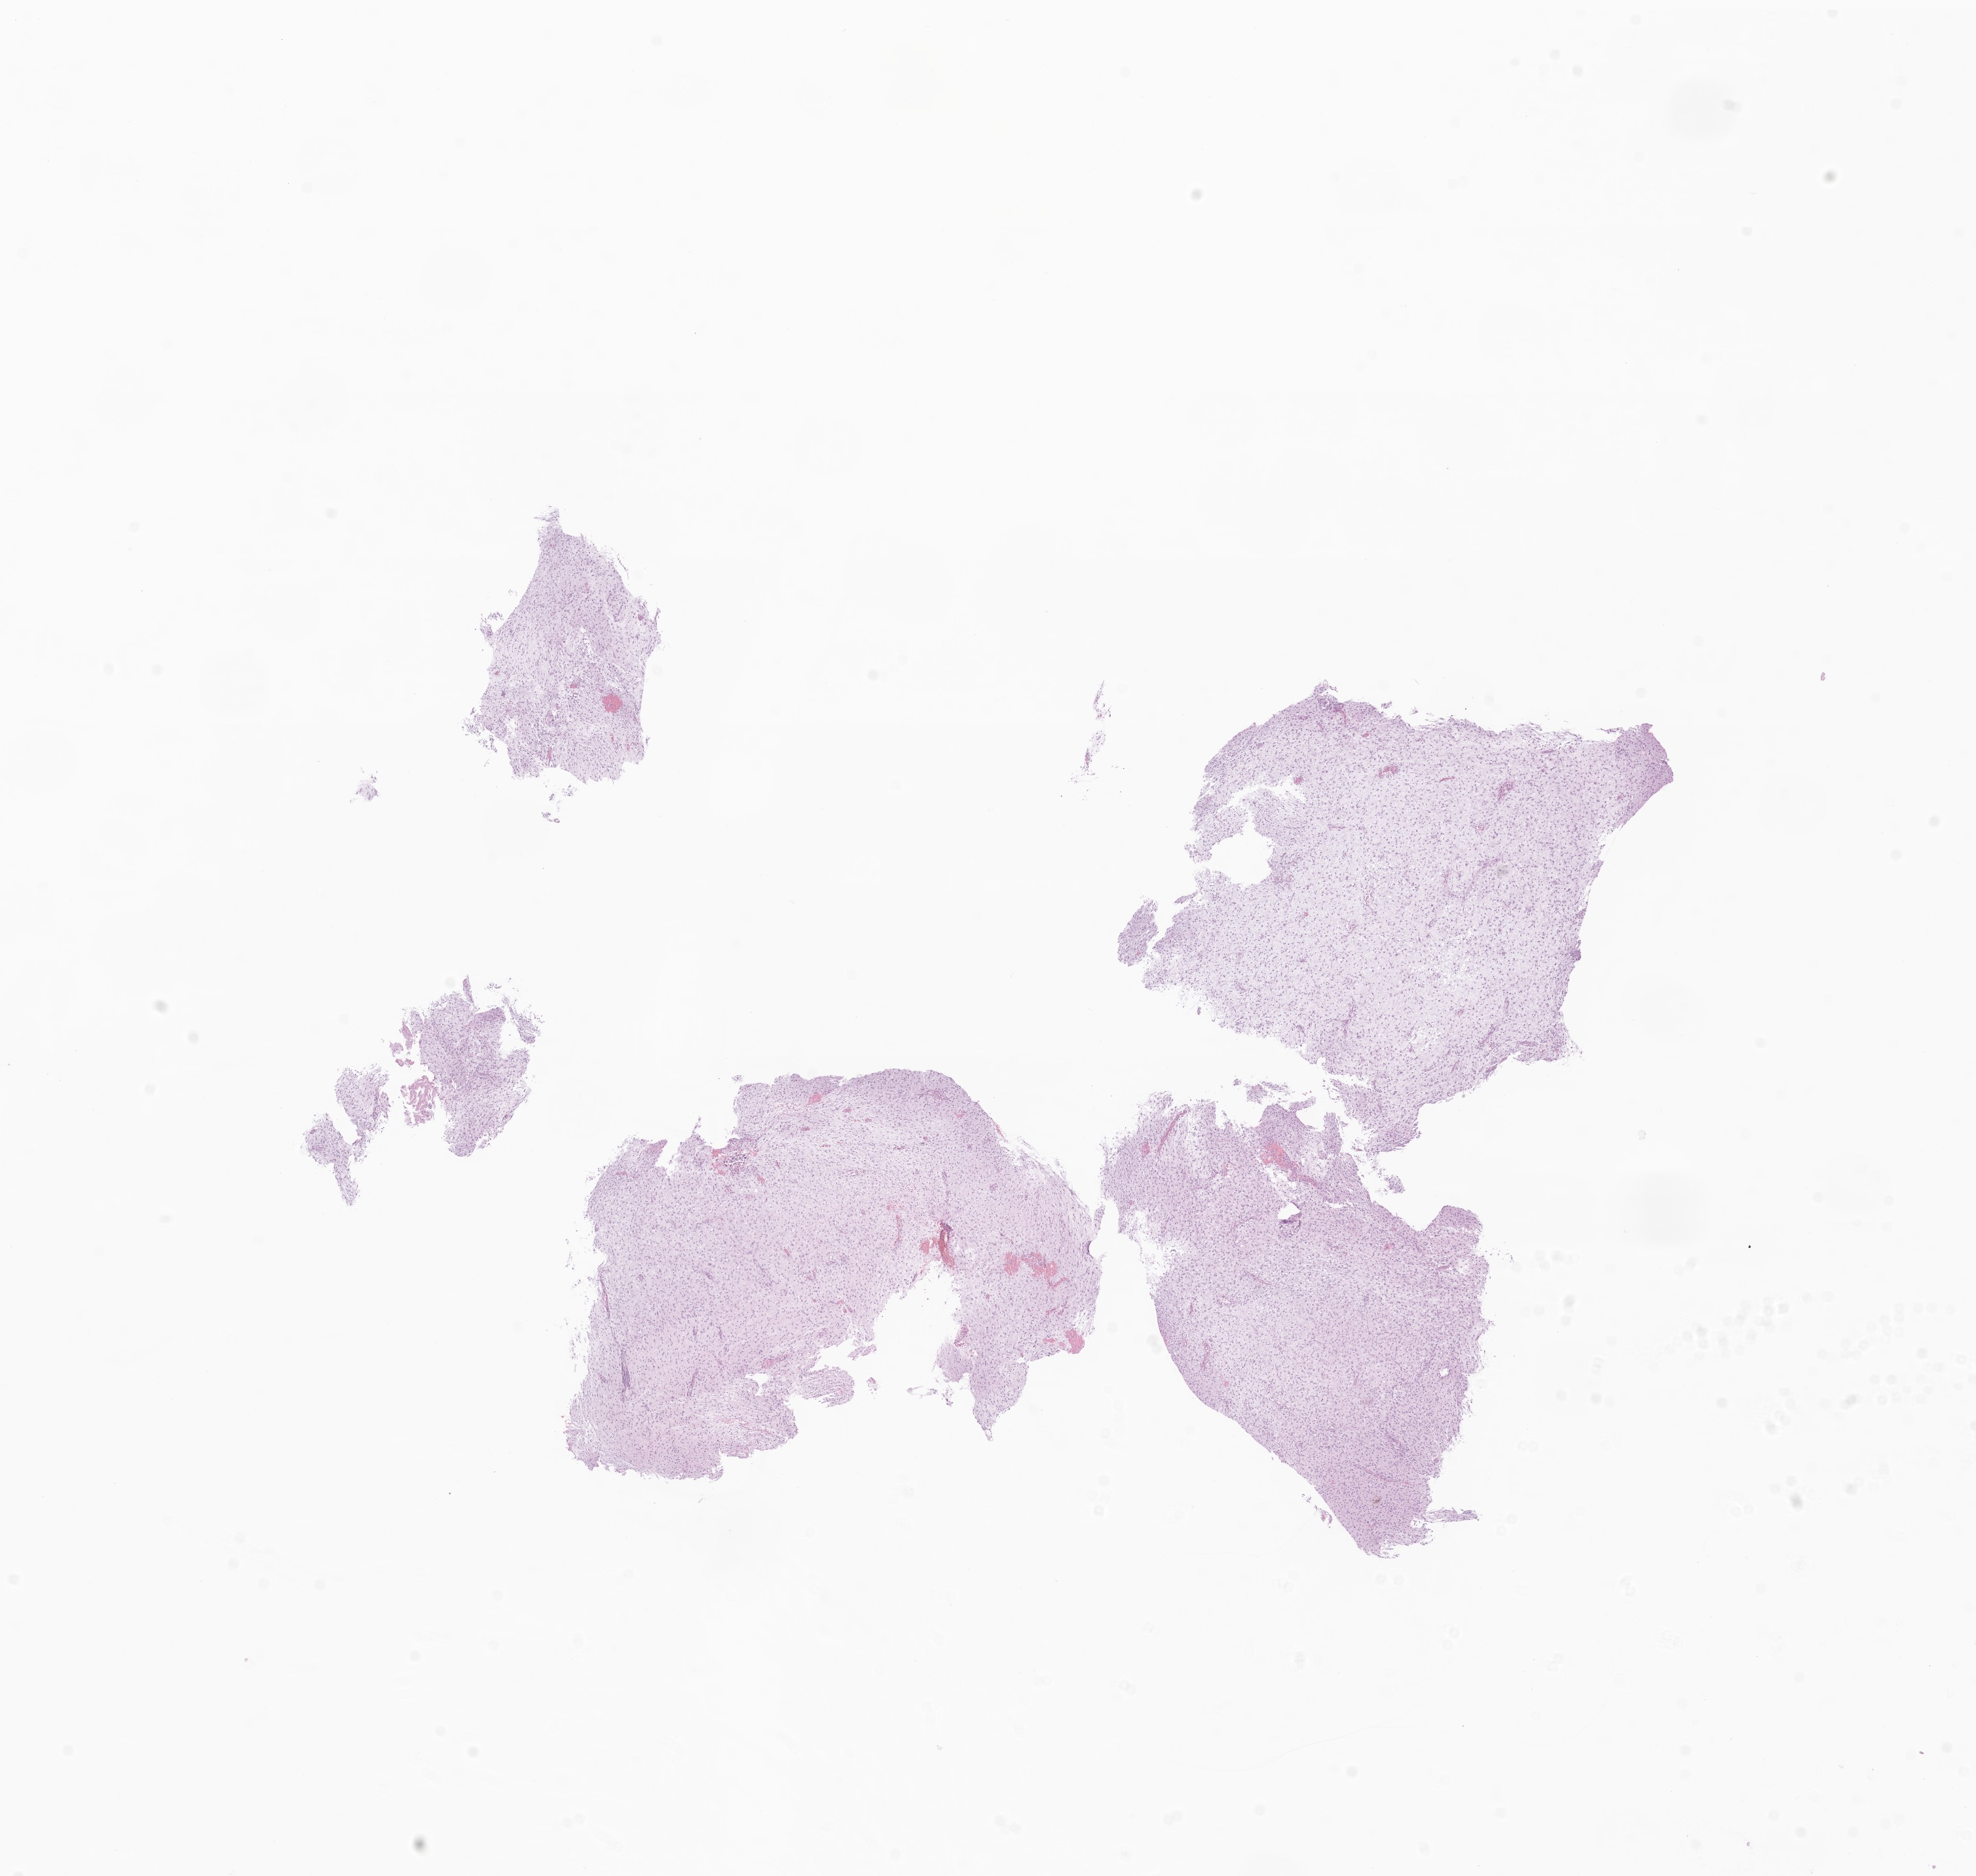
Hematoxylin and eosin (H&E) whole-slide image of tumor tissue from the cerebellum, whole scanned area (about 12.7 x 12.1 mm) shown as a low-resolution overview; formalin-fixed, paraffin-embedded (FFPE) tissue. Male patient, age 549 days.
• diagnosis (ICD-O-3 morphology term): Astrocytoma, NOS